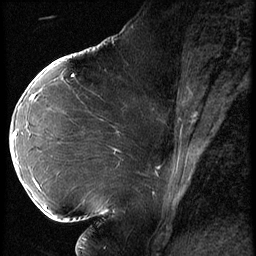
Breast MRI (dynamic contrast-enhanced), one sagittal slice. Position 31 of 62 along the scan axis. 3 images stored at this slice position (order not interpretable as contrast timing). 1.5 T. TE 4.2 ms, TR 9 ms. 2.5 mm slice thickness. 256 × 256 image matrix, field of view 180 × 180 mm. Female patient, age 43 years. From the clinical record (not read from this slice): setting: breast cancer imaged before/during neoadjuvant chemotherapy; receptor status: HER2-positive.
Outlined on this slice (semi-automatic segmentation, software-assisted and operator-edited):
- analysis volume of interest (the breast-tissue region the enhancement analysis was run in; not a lesion): bounding box (x1, y1, x2, y2) in pixels: (10, 90, 82, 203)
- tumour enhancement mask (voxels above the 140 % enhancement threshold inside the analysis volume of interest): (15, 95, 34, 136)